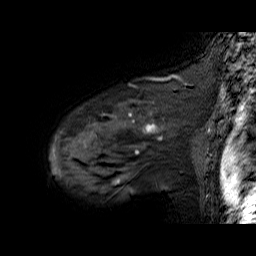
Breast MRI (dynamic contrast-enhanced), one sagittal slice. Slice 51 of 60 in the series (ordered by position). Dynamic contrast-enhanced series, time point 2 of 6 at this slice position (early post-contrast). 1.5 T. TE 6.3 ms, TR 32.9 ms. 4 mm slice thickness. 256 × 256 image matrix. Female patient. From the clinical record (not read from this slice): setting: breast cancer imaged before/during neoadjuvant chemotherapy; receptor status: HER2-positive.
Outlined on this slice (semi-automatically segmented with operator editing):
- analysis volume of interest (the breast-tissue region the enhancement analysis was run in; not a lesion): bounding box [x1, y1, x2, y2] px = [50, 92, 195, 174]
- tumour enhancement mask (voxels above the 100 % enhancement threshold inside the analysis volume of interest): [53, 112, 163, 174]